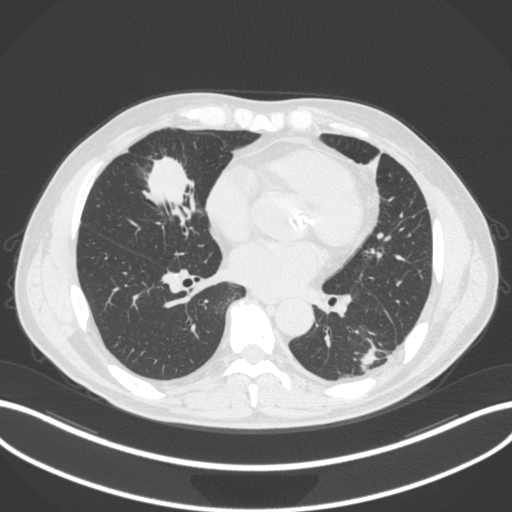
Chest CT, one axial slice; position 124 of 399 along the scan axis; reconstruction kernel B31f; 120 kVp; lung window (W 1500 / L -600 HU); 512 × 512 image matrix. Patient: male, 59 years. Case-level facts recorded for this patient, not image findings: clinical TNM (as recorded): T2a N1 M0.
Outlined on this slice (rectangle marked by the reading radiologist):
- lung tumour (recorded histology: adenocarcinoma): bounding box <135,149,201,225> (left, top, right, bottom; pixels)